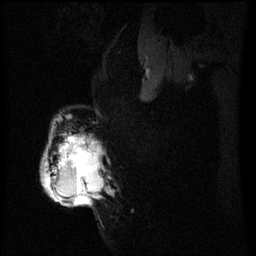
Breast MRI (dynamic contrast-enhanced), one sagittal slice; slice 43 of 60 in the series (ordered by position); dynamic contrast-enhanced series, image 2 of 3 at this slice position (ordered by acquisition); 1.5 T; TE 4.2 ms, TR 8 ms; 256 × 256 image matrix, field of view 200 × 200 mm. Female patient, age 50 years.
Outlined on this slice (semi-automatic segmentation, software-assisted and operator-edited):
- analysis volume of interest (the breast-tissue region the enhancement analysis was run in; not a lesion): bounding box [x1, y1, x2, y2] px = [42, 132, 105, 207]
- tumour enhancement mask (voxels above the 70 % enhancement threshold inside the analysis volume of interest): [45, 136, 100, 207]